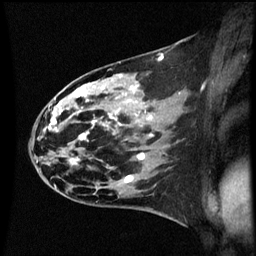
Breast MRI (dynamic contrast-enhanced), one sagittal slice. Position 34 of 60 along the scan axis. Dynamic contrast-enhanced series, image 2 of 3 at this slice position (ordered by acquisition). 1.5 T. TE 4.2 ms, TR 8.9 ms. 2 mm slice thickness. 256 × 256 image matrix, field of view 200 × 200 mm. Female patient, age 44 years. Case-level facts recorded for this patient, not image findings: setting: breast cancer imaged before/during neoadjuvant chemotherapy; receptor status: HR-positive, HER2-negative.
Outlined on this slice (semi-automatically segmented with operator editing):
- analysis volume of interest (the breast-tissue region the enhancement analysis was run in; not a lesion): bounding box [x1, y1, x2, y2] px = [43, 78, 153, 189]
- tumour enhancement mask (voxels above the 70 % enhancement threshold inside the analysis volume of interest): [48, 88, 145, 181]